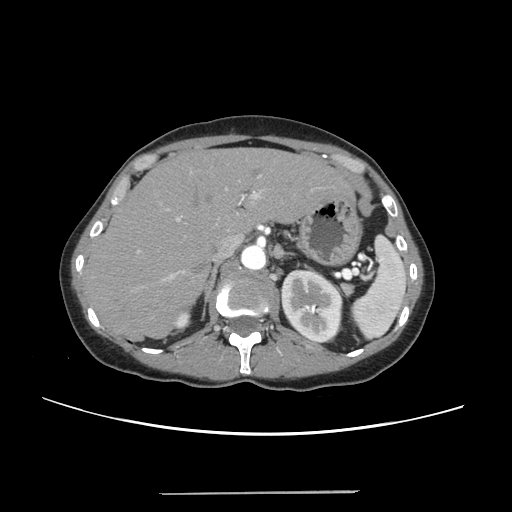
Contrast-enhanced abdominal CT, one axial slice. Position 168 of 240 along the scan axis. Soft-tissue window (W 400 / L 40 HU). 512 × 512 image matrix, field of view 371 × 371 mm. Female patient, age 60 years. Case-level facts recorded for this patient, not image findings: diagnosis: colorectal cancer liver metastases, imaged before liver resection; multiple liver metastases: no.
Structures marked on this image (manually delineated by an expert):
- liver: bounding box <86,149,349,337> (left, top, right, bottom; pixels)
- planned liver remnant (the part of the liver to remain after resection): <86,149,348,337>
- portal vein (with intrahepatic branches): <137,172,265,282>